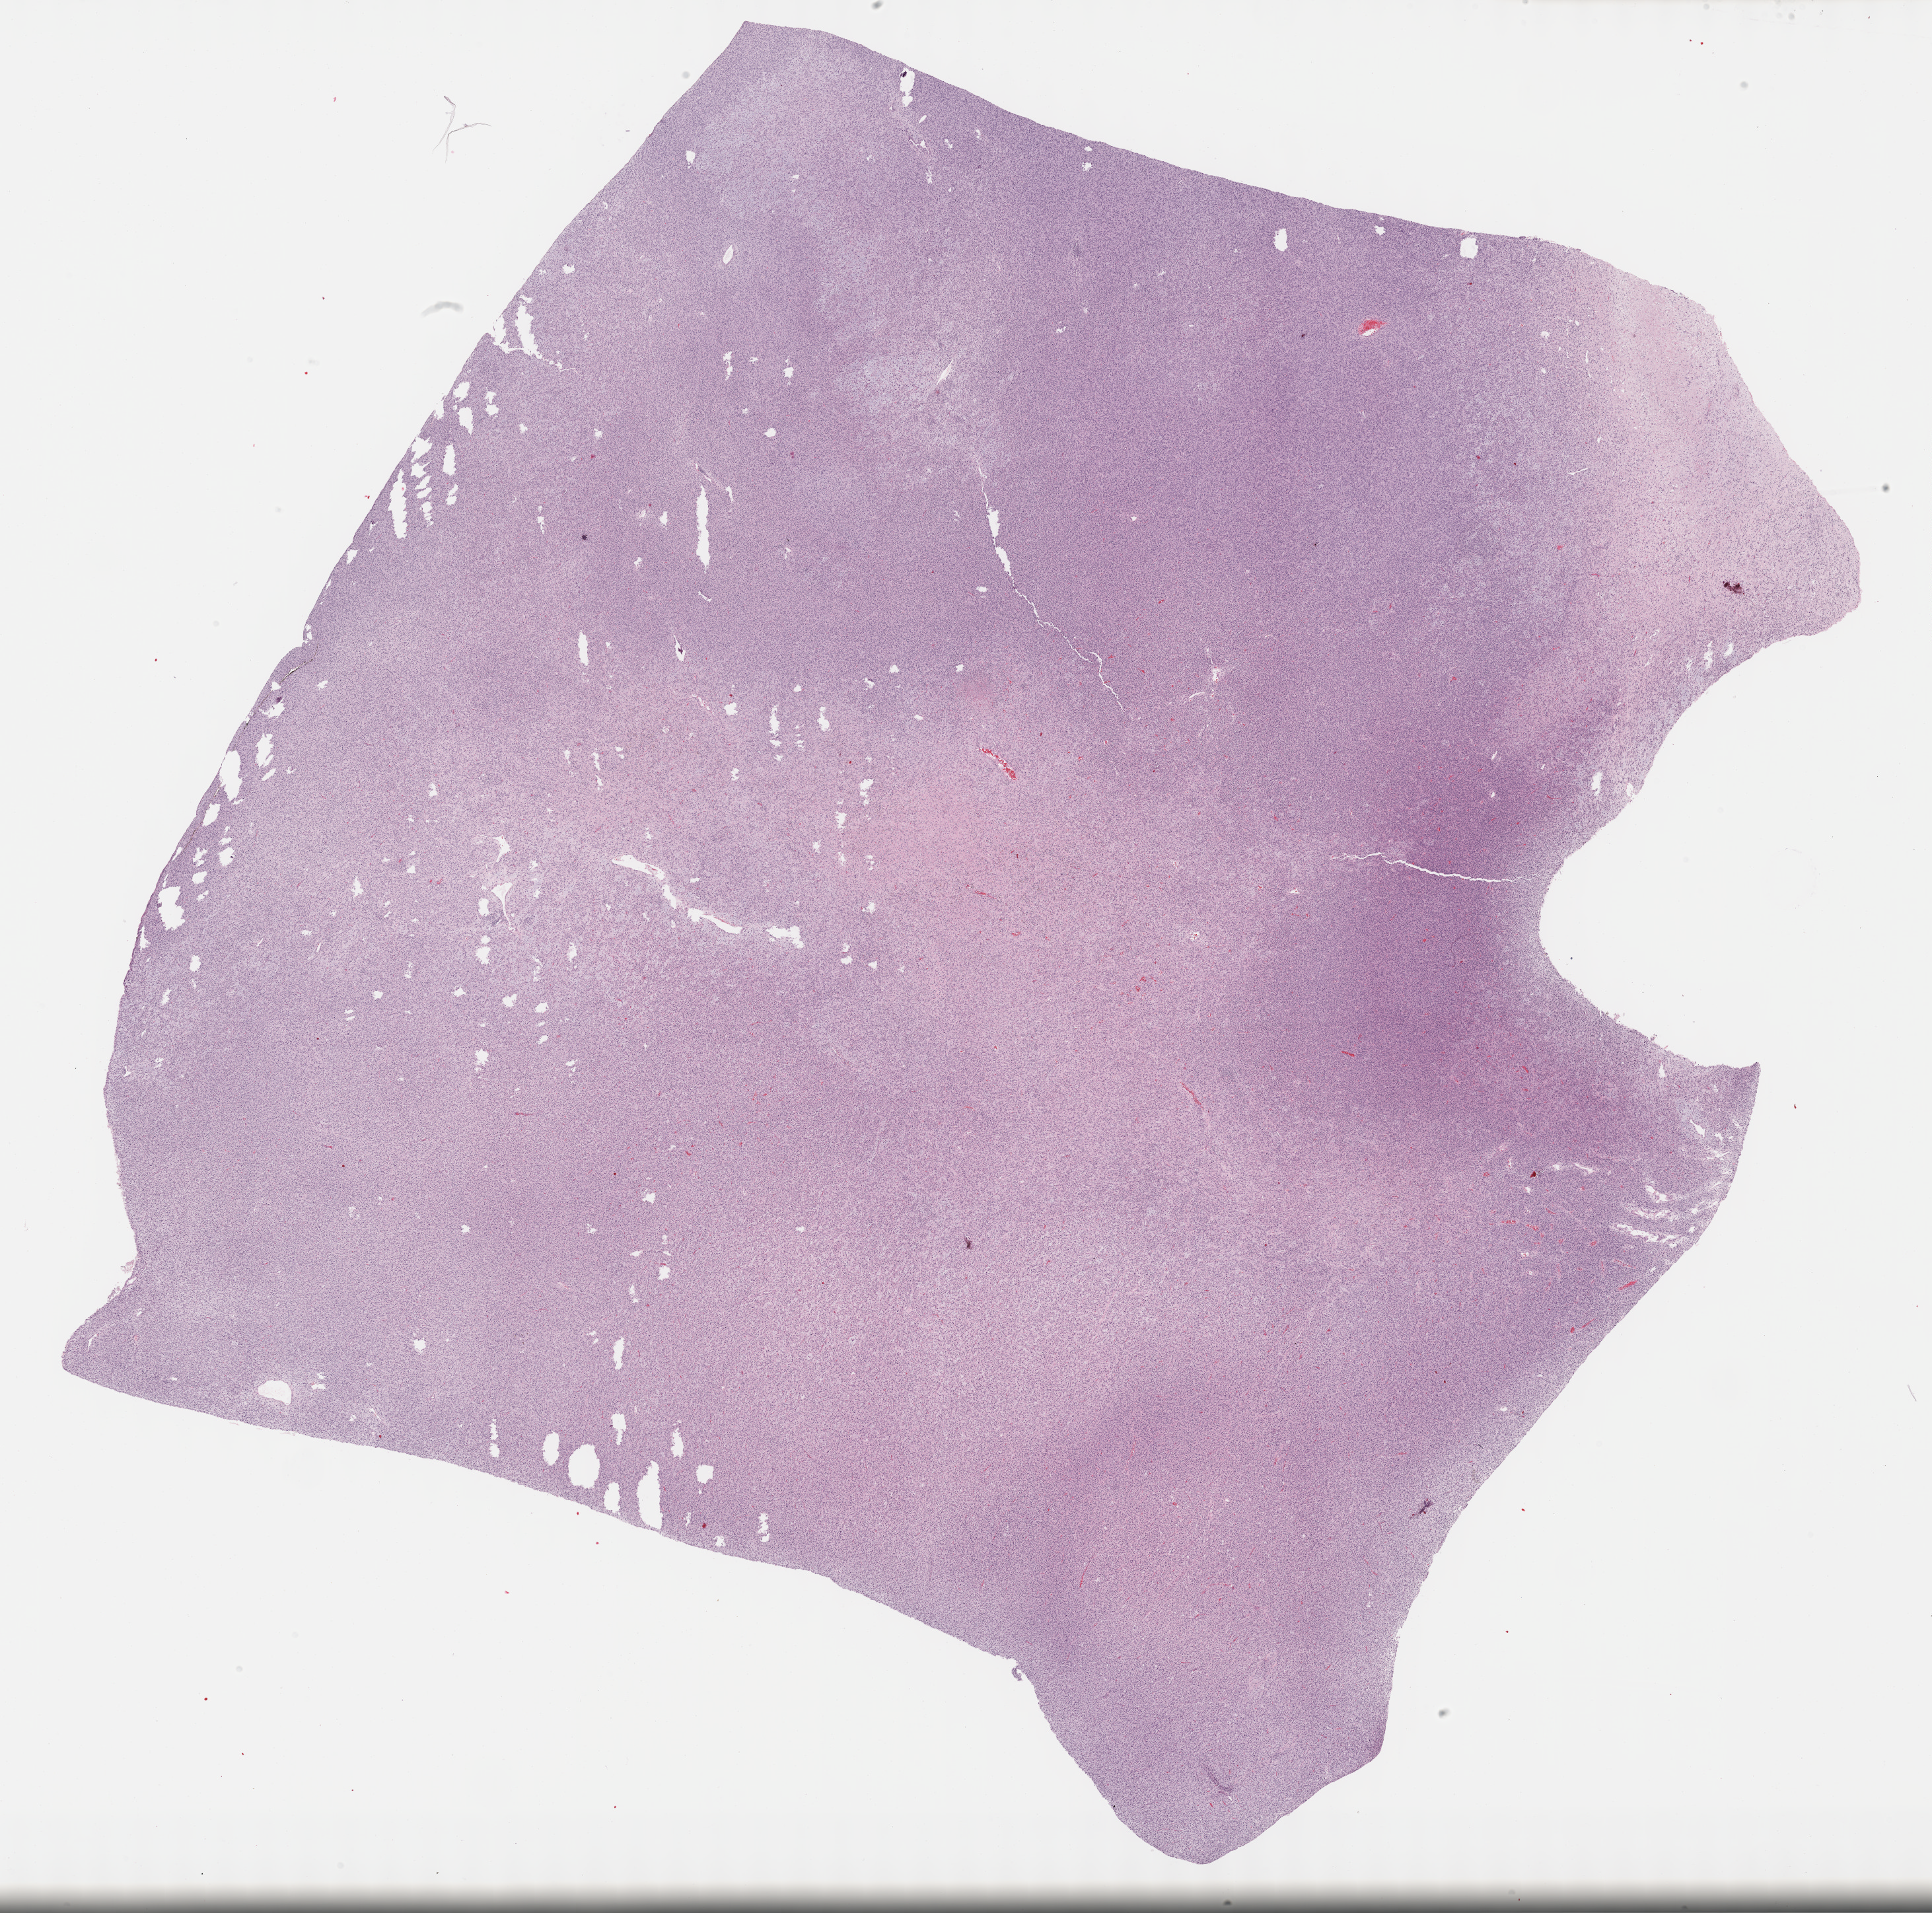
Digitized H&E-stained tissue section (whole slide), whole scanned area (about 23.7 x 23.4 mm) shown as a low-resolution overview; formalin-fixed paraffin-embedded (FFPE) diagnostic section; sample: primary tumour, retroperitoneum and peritoneum. Male patient; age at initial diagnosis 52 years.
Histologic diagnosis: Dedifferentiated liposarcoma (retroperitoneum).